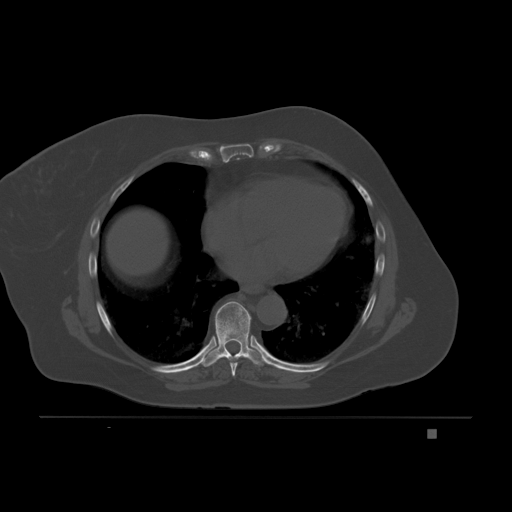
CT including the spine, one axial slice. Slice 121 of 221 in the series (ordered by position). Bone window (W 1800 / L 400 HU). 3 mm slice thickness. 512 × 512 image matrix, field of view 474 × 474 mm. Patient: female, 63 years. Case-level facts recorded for this patient, not image findings: primary cancer: breast.
Outlined on this slice (semi-automatic segmentation, software-assisted and operator-edited):
- T7 vertebra: bounding box (x1, y1, x2, y2) in pixels: (229, 361, 238, 377)
- T8 vertebra: (203, 301, 264, 367)